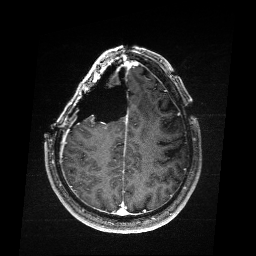
Brain MRI from a brain-tumour surgery series, one axial slice; position 65 of 176 along the scan axis; T1-weighted post-contrast; 1 mm slice thickness; 256 × 256 image matrix, field of view 256 × 256 mm. Case-level facts recorded for this patient, not image findings: histopathology: Astrocytoma; WHO grade: 4; IDH mutation: yes.
Structures marked on this image (expert manual segmentation):
- residual tumour: bounding box <91,118,94,122> (left, top, right, bottom; pixels)